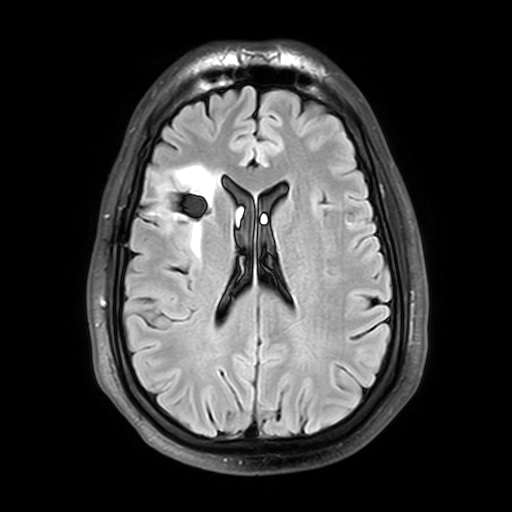
Brain MRI from a brain-tumour surgery series, one axial slice. Position 17 of 42 along the scan axis. T2 FLAIR. 512 × 512 image matrix. From the clinical record (not read from this slice): histopathology: Astrocytoma; WHO grade: 2; IDH mutation: yes; tumour location: Right Insular.
Annotated regions visible in this slice (manually delineated by an expert):
- tumour: box from (x=137, y=166) to (x=223, y=258) px